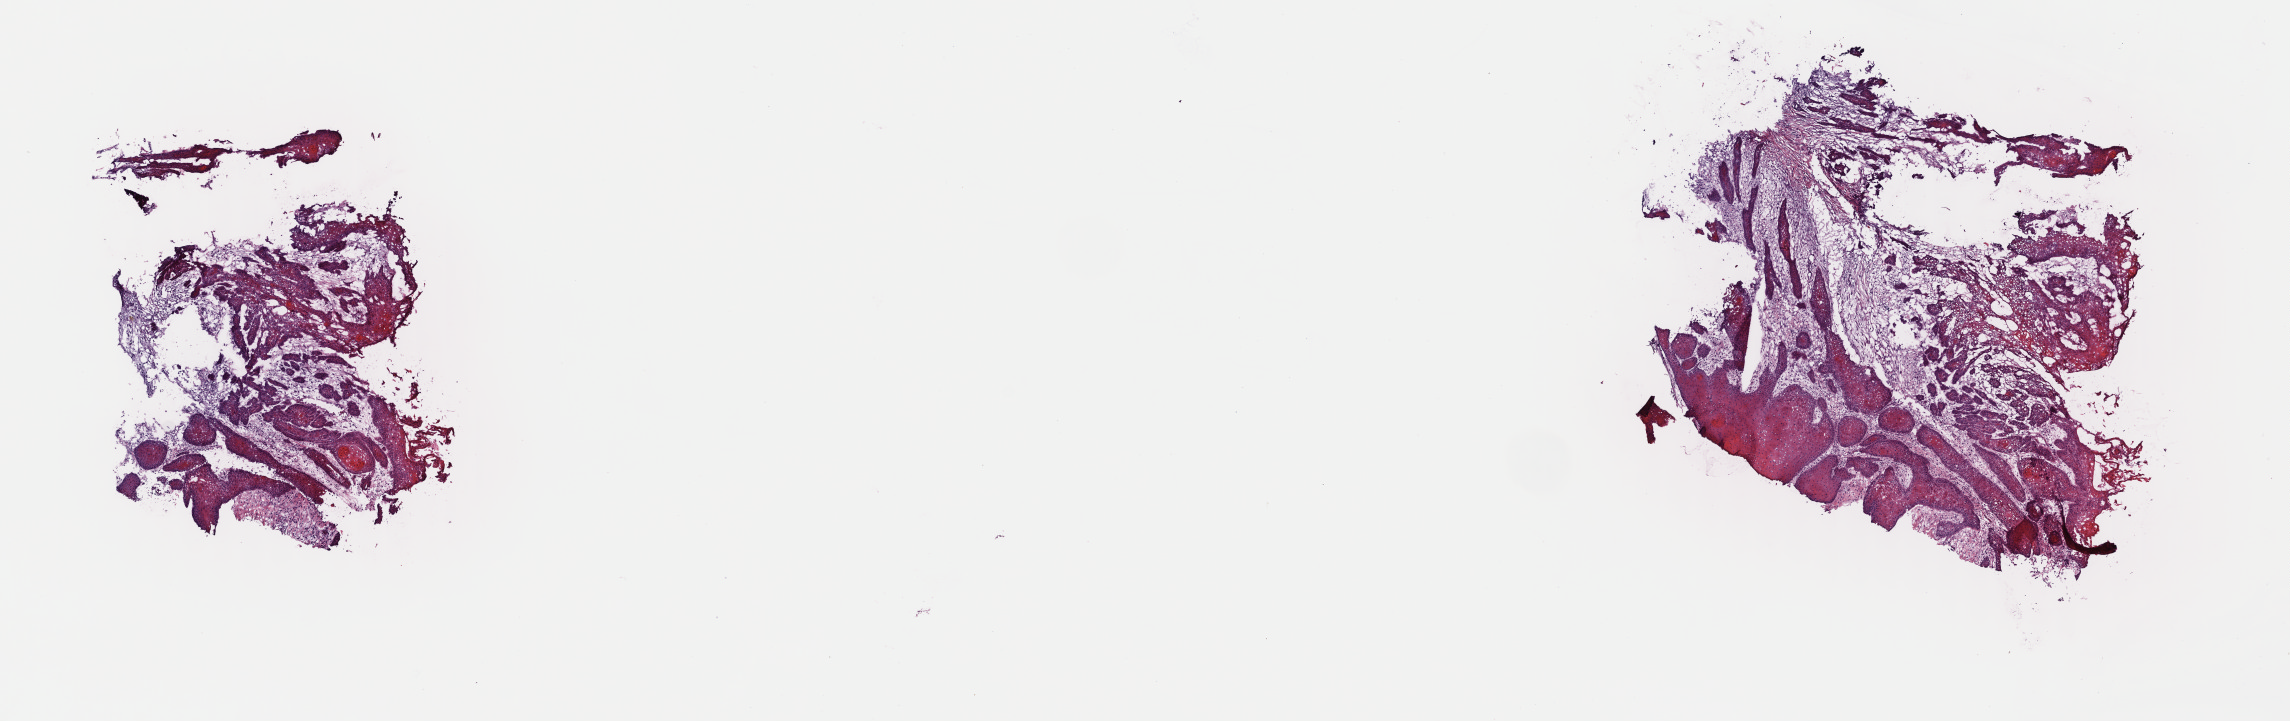
Digitized H&E-stained tissue section (whole slide), low-resolution overview of the scanned area, about 18.1 x 5.7 mm (acquisition: 40x scan), frozen section from the top of the tissue portion, head and neck, primary tumour sample. Male, age 82 years at initial diagnosis. Pathologist review of this section (percent, as recorded): tumour cells 100%, tumour nuclei 65%.
Pathologic diagnosis: Squamous cell carcinoma, keratinizing, NOS (gum, NOS).